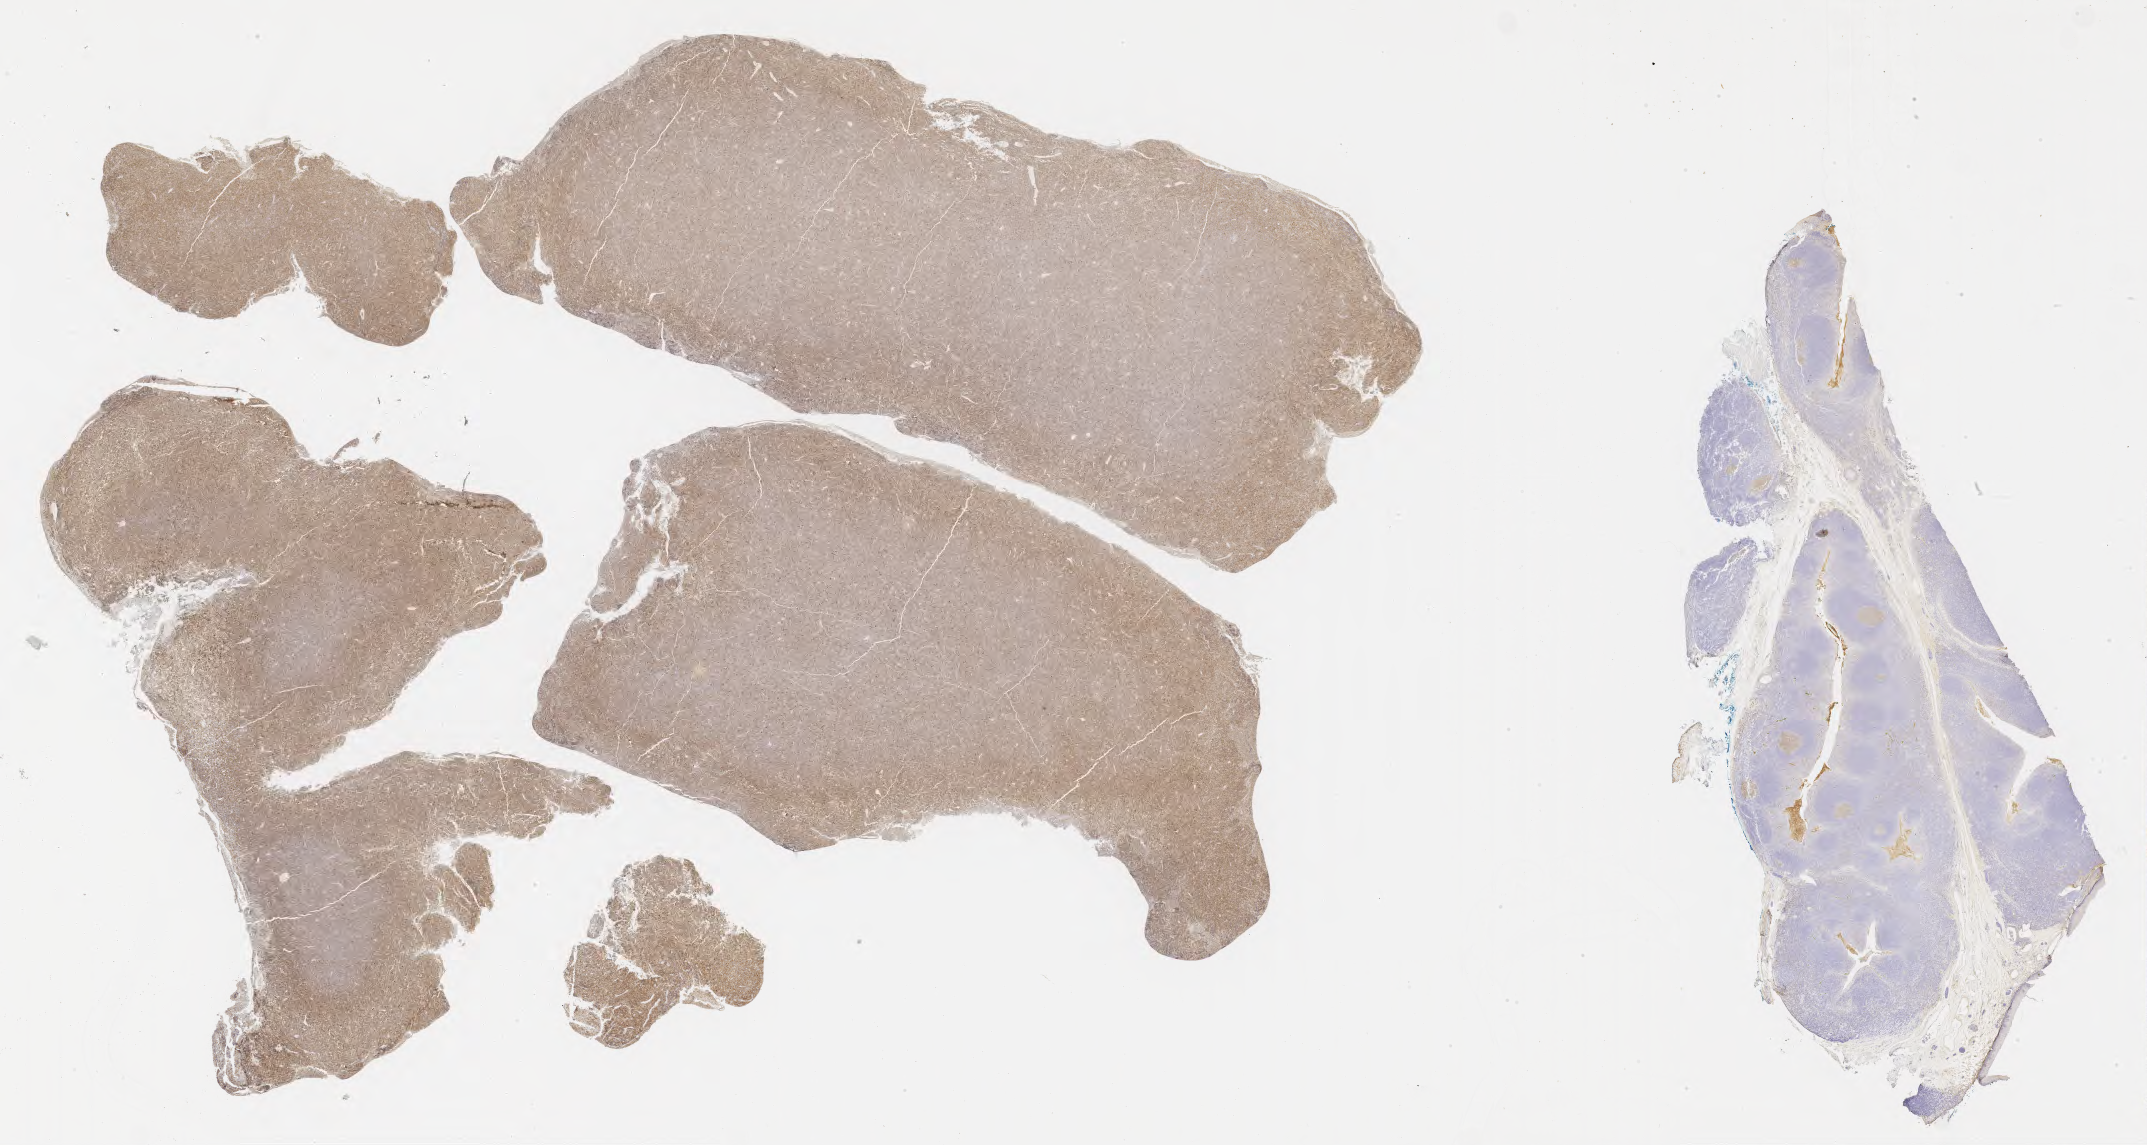
Immunohistochemistry (IHC) whole-slide image stained for CD10, a low-resolution overview of the entire scanned area, about 34.7 x 18.5 mm. Specimen: tumor tissue. Site: peritoneum. Female, age 7 years at initial diagnosis.
Diagnosis: Burkitt lymphoma, NOS.